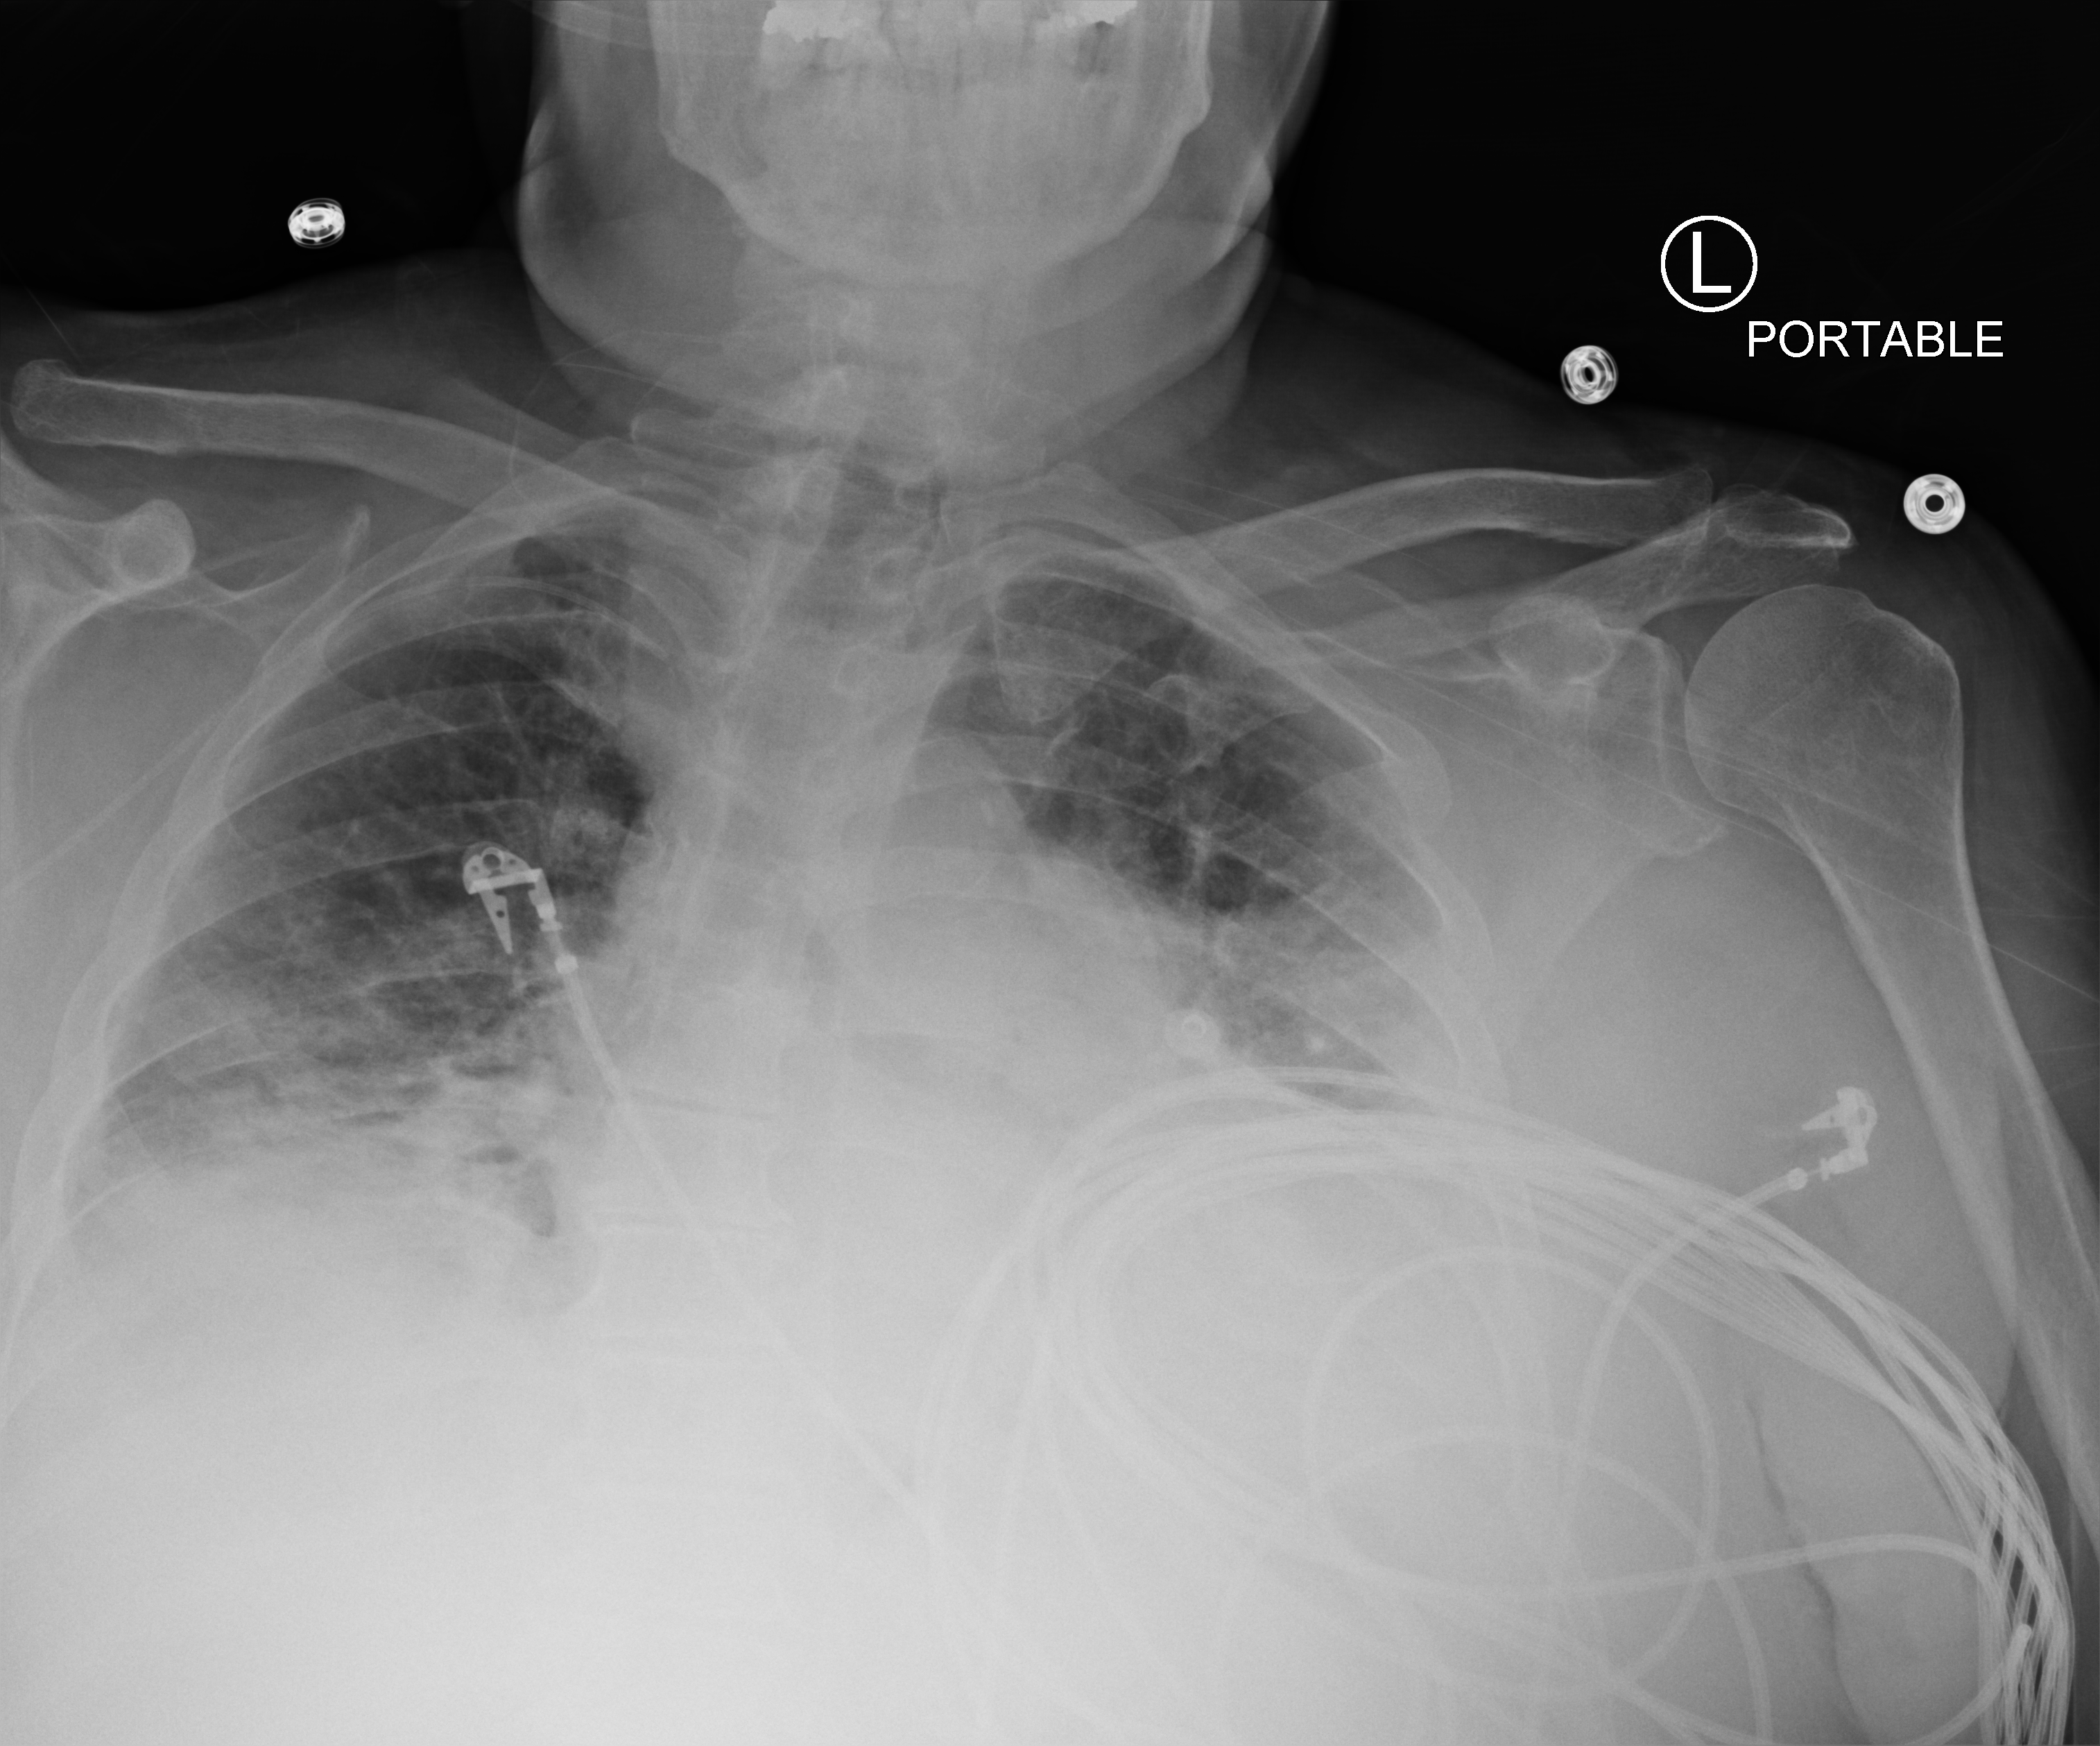
Chest X-ray (portable), anteroposterior (AP) projection. Patient hospitalised with COVID-19; male, aged 60–74 years.
Admission-level facts for this patient (not findings on this image; timing relative to this image not recorded): mechanically ventilated during this hospital stay: yes; admitted to intensive care during this hospital stay: yes.